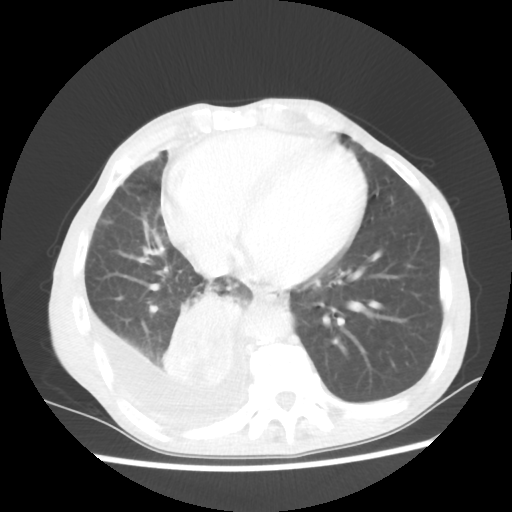
Chest CT, one axial slice; position 21 of 60 along the scan axis; lung window (W 1500 / L -600 HU); 5 mm slice thickness; 512 × 512 image matrix, field of view 335 × 335 mm. Male patient, age 76 years. Case-level facts recorded for this patient, not image findings: clinical TNM (as recorded): T3 N3 M1a; histopathological grade: G3.
Structures marked on this image (rectangle marked by the reading radiologist):
- lung tumour (recorded histology: squamous cell carcinoma): bounding box [x1, y1, x2, y2] px = [159, 280, 246, 389]